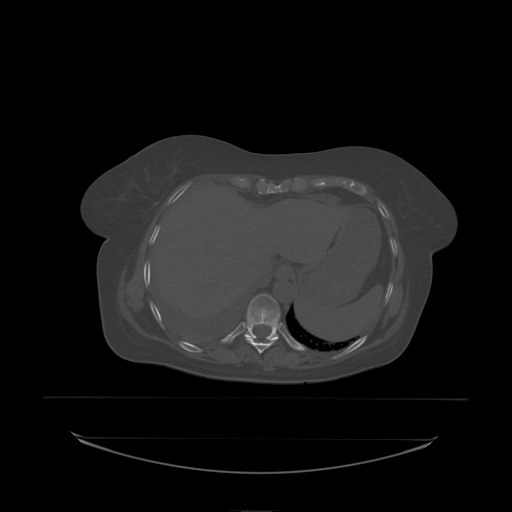
CT including the spine, one axial slice. Position 119 of 242 along the scan axis. Bone window (W 1800 / L 400 HU). 2.5 mm slice thickness. 512 × 512 image matrix. Female patient, age 53 years. From the clinical record (not read from this slice): primary cancer: lung; vertebrae with lytic lesions (as recorded): T7, L1.
Structures marked on this image (semi-automatically segmented with operator editing):
- T10 vertebra: bounding box [x1, y1, x2, y2] px = [245, 294, 281, 338]